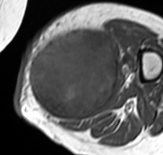
MRI of an extremity soft-tissue mass, one axial slice. Slice 30 of 65 in the series (ordered by position). MR volume resampled by the dataset authors to the PET/CT grid (not the native acquisition matrix). 3.27 mm slice thickness. 163 × 155 image matrix, field of view 159 × 151 mm. Female patient. From the clinical record (not read from this slice): histological type: pleomorphic leiomyosarcoma; grade: high; site of the primary tumour: left thigh.
Structures marked on this image (expert contour drawn on MRI and transferred to this co-registered scan by the dataset authors):
- gross tumour volume including surrounding oedema: bounding box [x1, y1, x2, y2] px = [28, 31, 118, 123]
- gross tumour volume (mass): [28, 31, 118, 121]